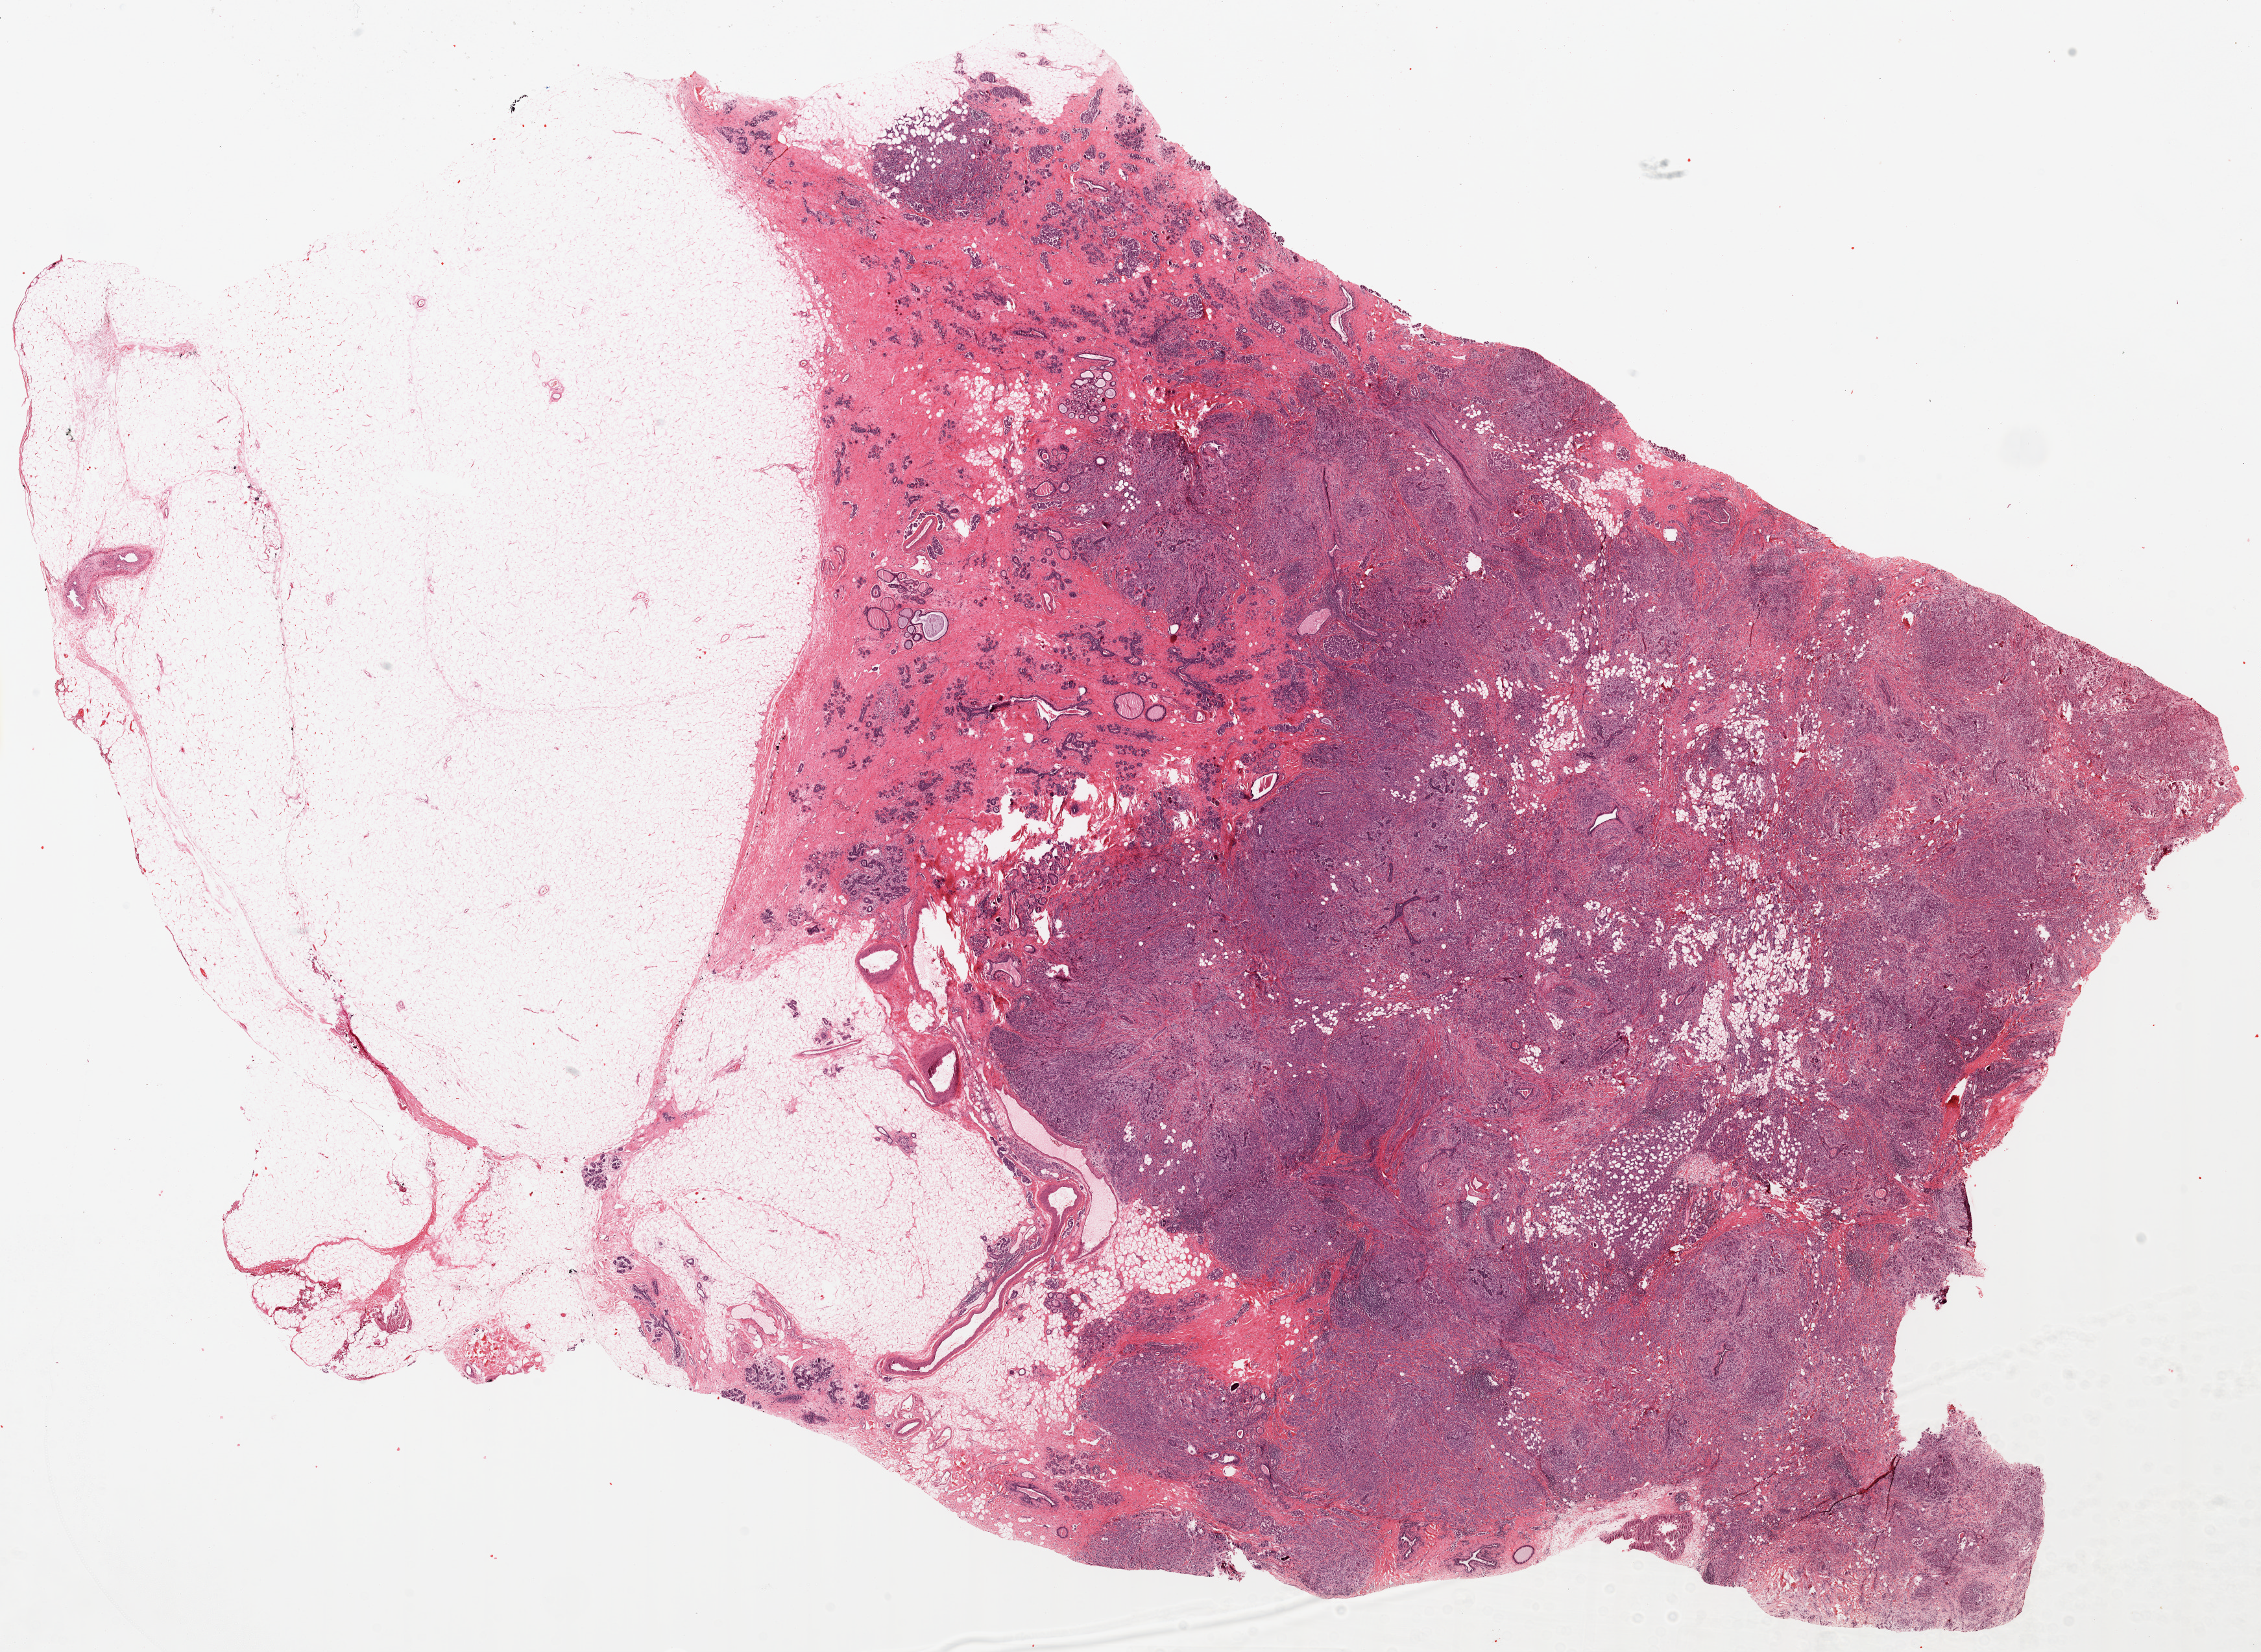
Whole-slide histology image, H&E, shown as a low-resolution overview of the whole scanned area (about 27.8 x 20.3 mm, from a 20x scan); formalin-fixed paraffin-embedded (FFPE) diagnostic section; breast, primary tumour sample. Female, age 34 years at initial diagnosis.
AJCC pathologic stage: IIIA. Diagnosis: Infiltrating duct carcinoma, NOS. Laterality: right. Lymph nodes positive (case pathology): 4 of 17 examined.